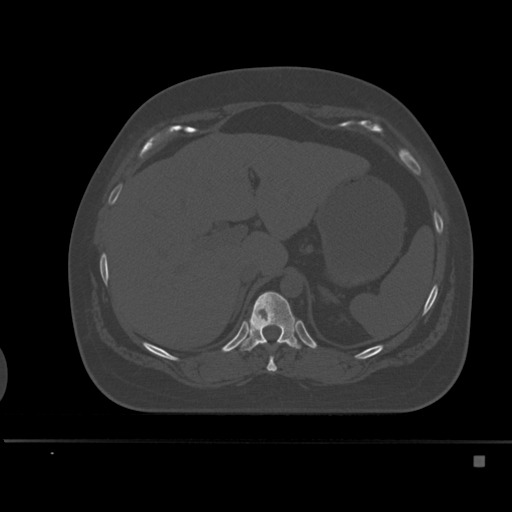
CT including the spine, one axial slice; position 236 of 495 along the scan axis; bone window (W 1800 / L 400 HU); 1.5 mm slice thickness; 512 × 512 image matrix, field of view 404 × 404 mm. Female patient, age 33 years. From the clinical record (not read from this slice): primary cancer: breast; vertebrae with lytic lesions (as recorded): T1.
Outlined on this slice (semi-automatic segmentation, software-assisted and operator-edited):
- T10 vertebra: bounding box [x1, y1, x2, y2] px = [267, 356, 277, 372]
- T11 vertebra: [237, 291, 305, 351]